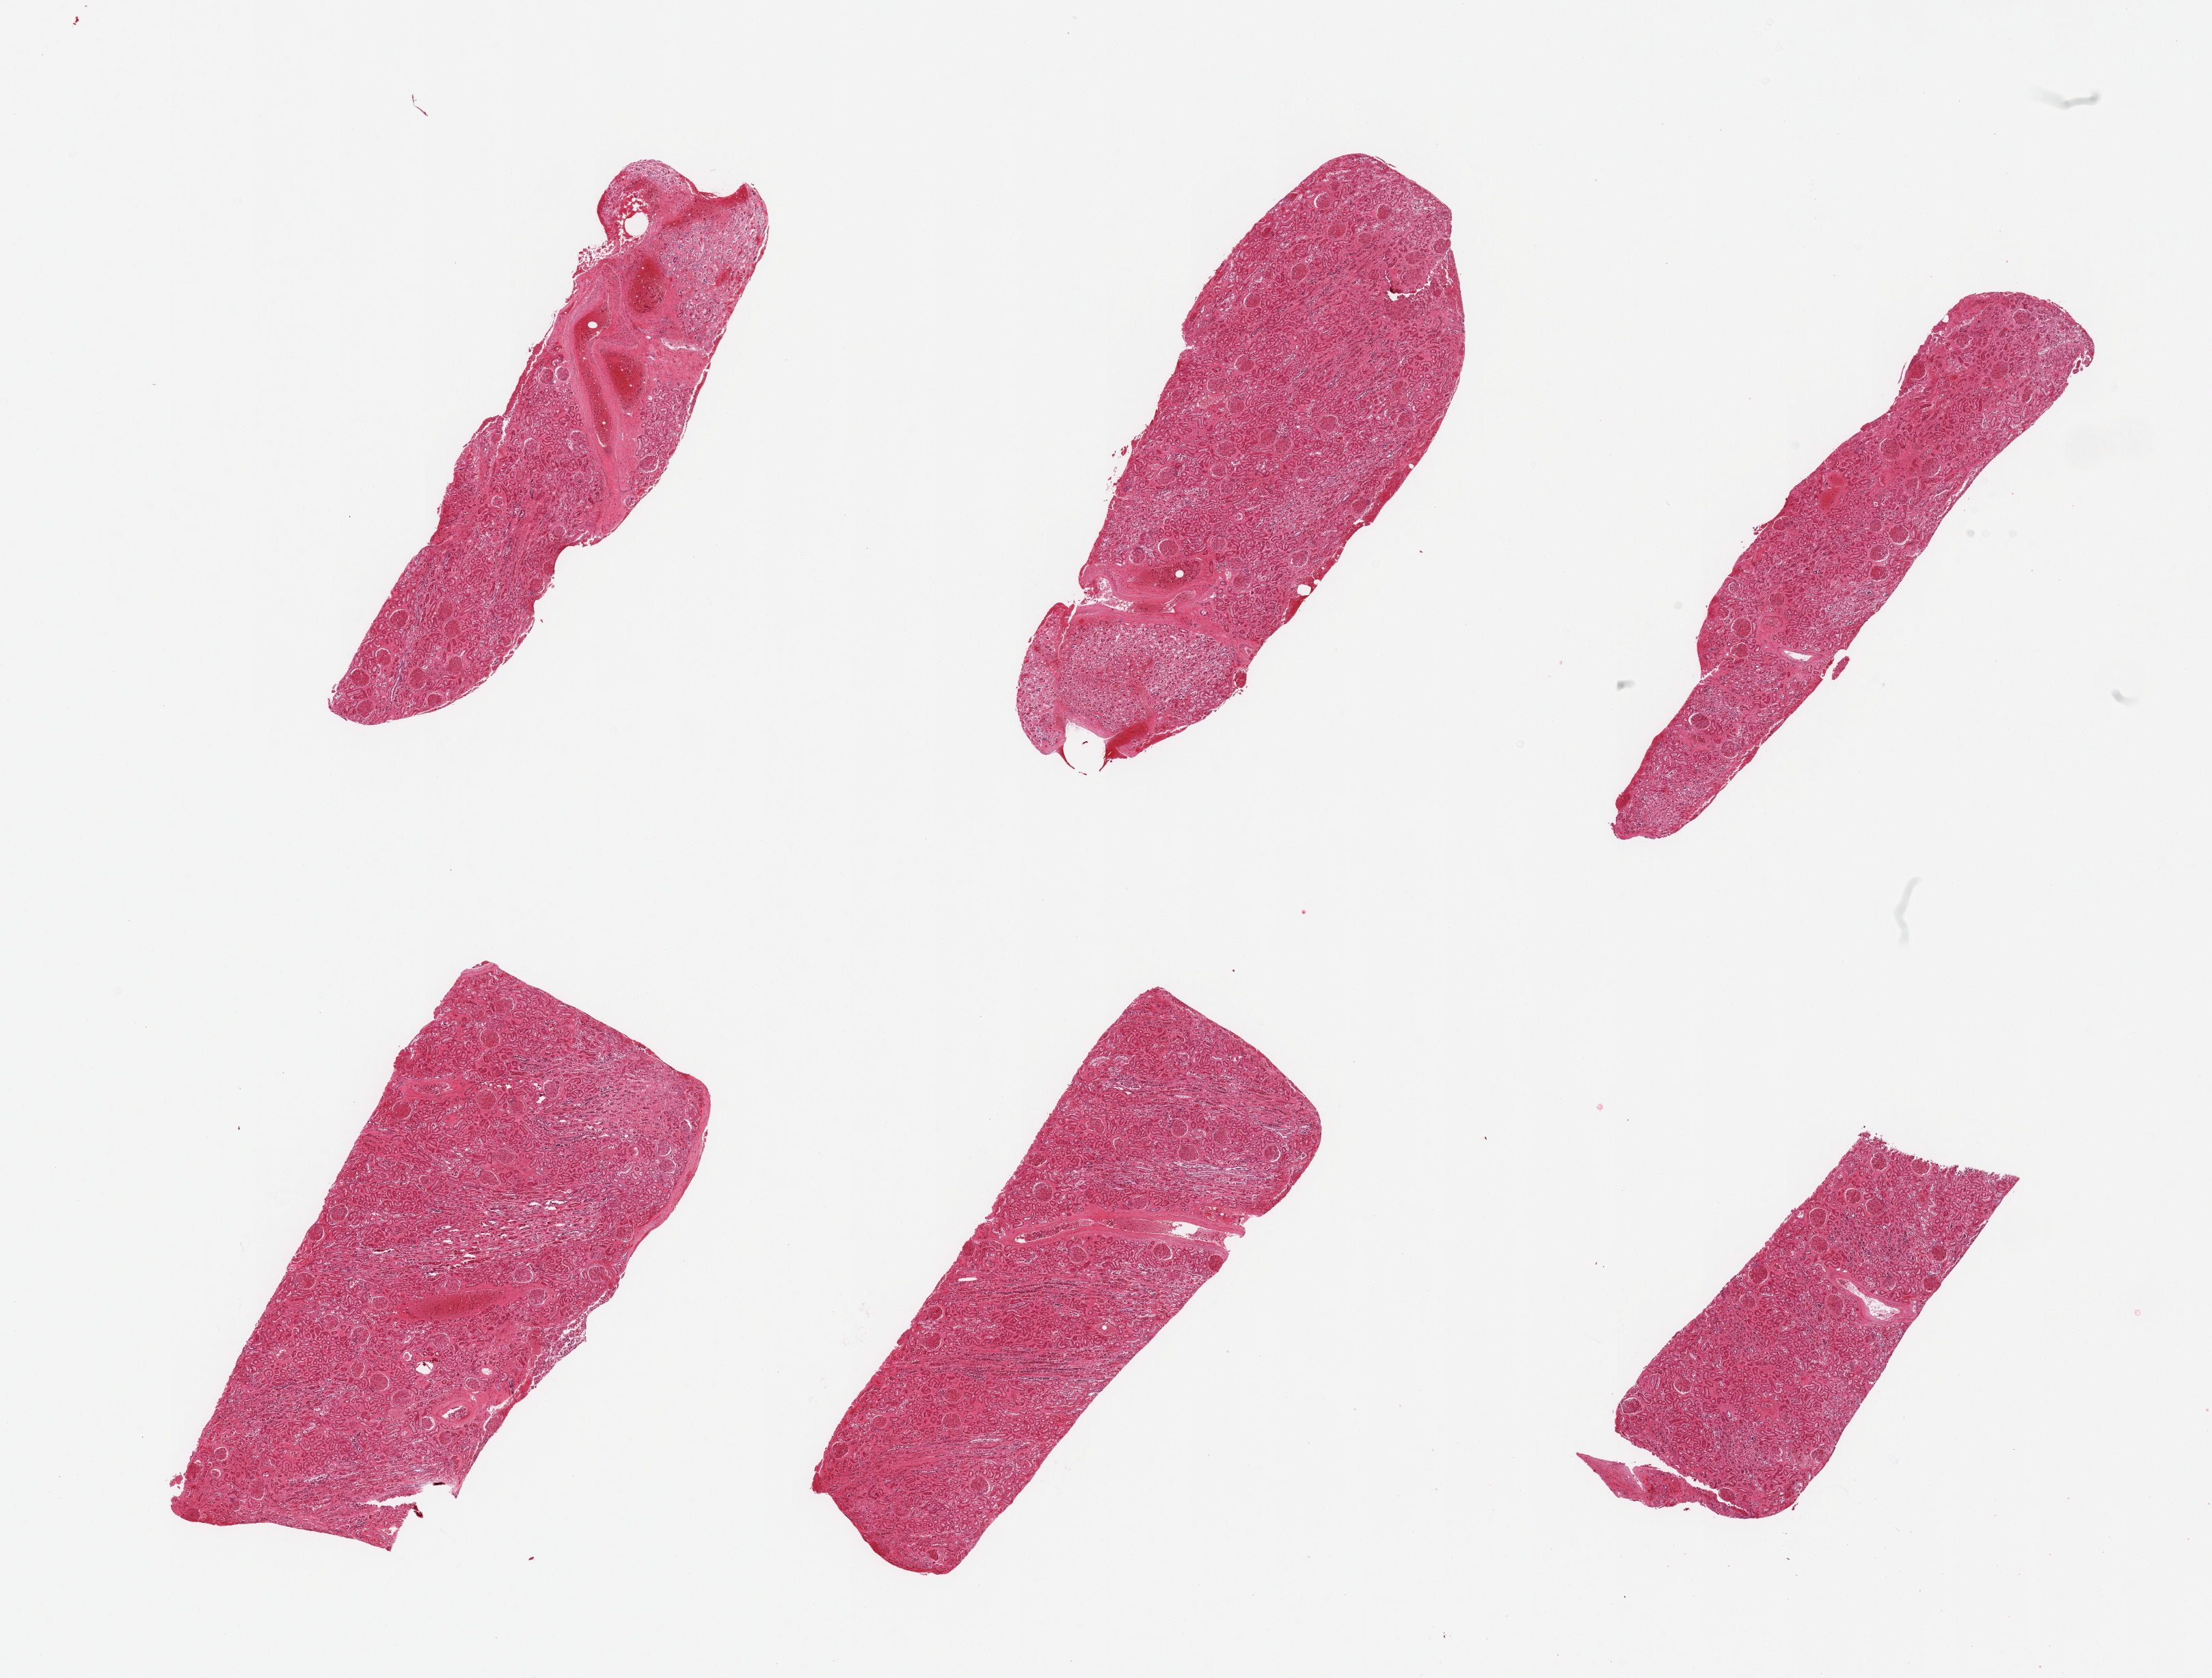
Hematoxylin and eosin (H&E) whole-slide image — low-resolution overview of the scanned area, about 25.6 x 19.4 mm (from a 20x scan). PAXgene-fixed, paraffin-embedded tissue. Sampled site (target tissue): renal cortex. Tissue donor sample. Male donor.
Reviewer comment on this tissue sample: 6 pieces; glomeruli in all sections, mild to moderate autolysis, includes portion of medulla.